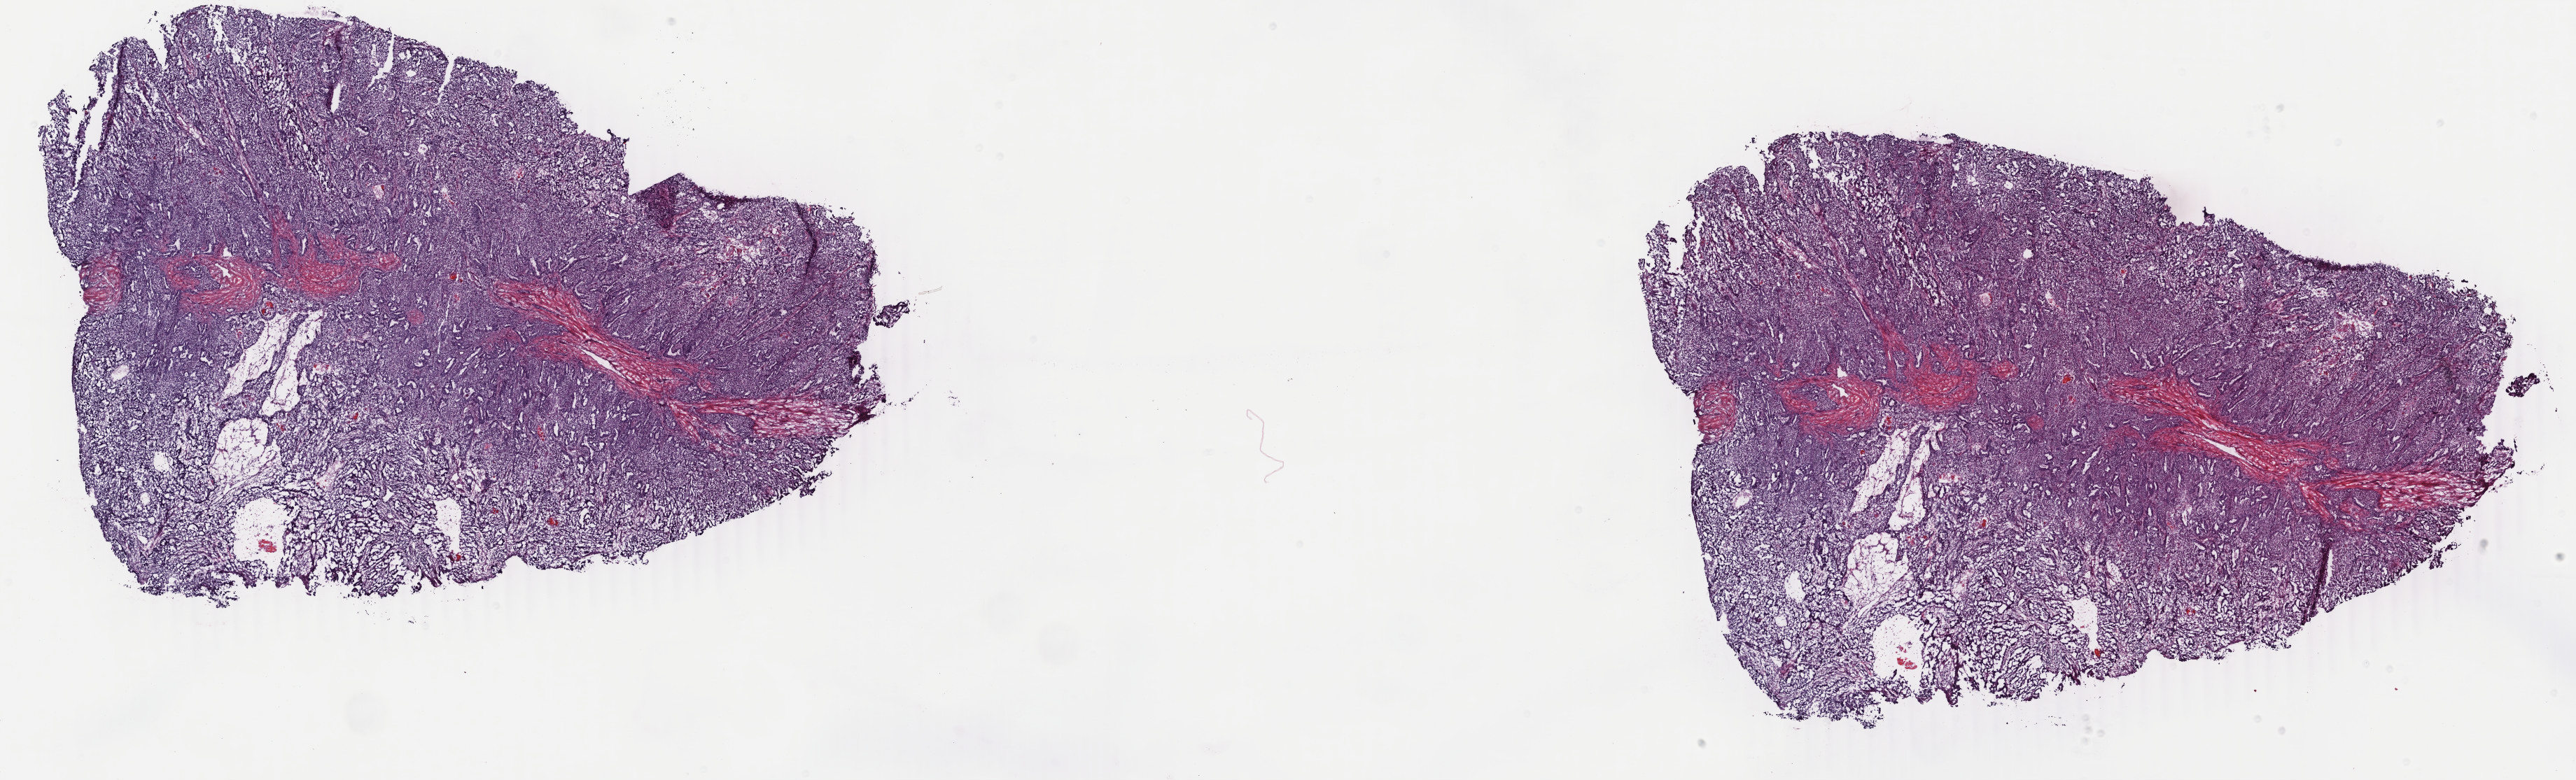
Hematoxylin and eosin (H&E) stained whole-slide image, low-resolution overview of the scanned area, about 29.3 x 8.9 mm, frozen section from the bottom of the tissue portion, uterus, primary tumour sample. Female, age 48 years at initial diagnosis. Histologic grade: G1 (well differentiated). Composition of this section per pathologist review: tumour cells 70%, tumour nuclei 80%, normal cells 10%, stromal cells 10%, necrosis 10%. Infiltration values recorded for this section: lymphocyte infiltration 30%, monocyte infiltration 0%, neutrophil infiltration 10%.
- pathologic diagnosis: Endometrioid adenocarcinoma, NOS (endometrium)
- FIGO stage: IA